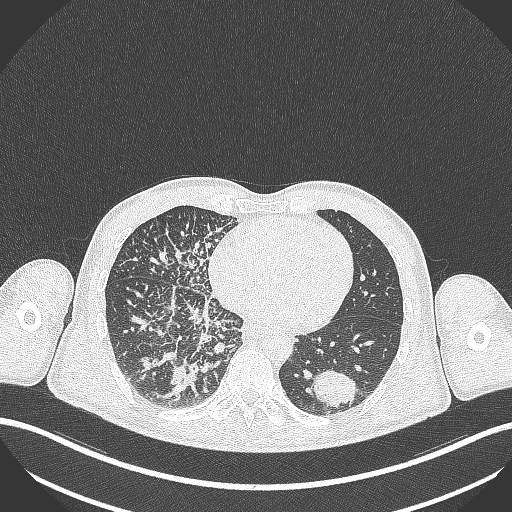
Chest CT, one axial slice. Position 109 of 348 along the scan axis. Reconstruction kernel B70f. Lung window (W 1500 / L -600 HU). 1 mm slice thickness. 512 × 512 image matrix, field of view 400 × 400 mm. Patient: male, 49 years. Case-level facts recorded for this patient, not image findings: clinical TNM (as recorded): T2b N1 M0.
Outlined on this slice (rectangle marked by the reading radiologist):
- lung tumour (recorded histology: adenocarcinoma): bounding box [x1, y1, x2, y2] px = [308, 366, 358, 407]